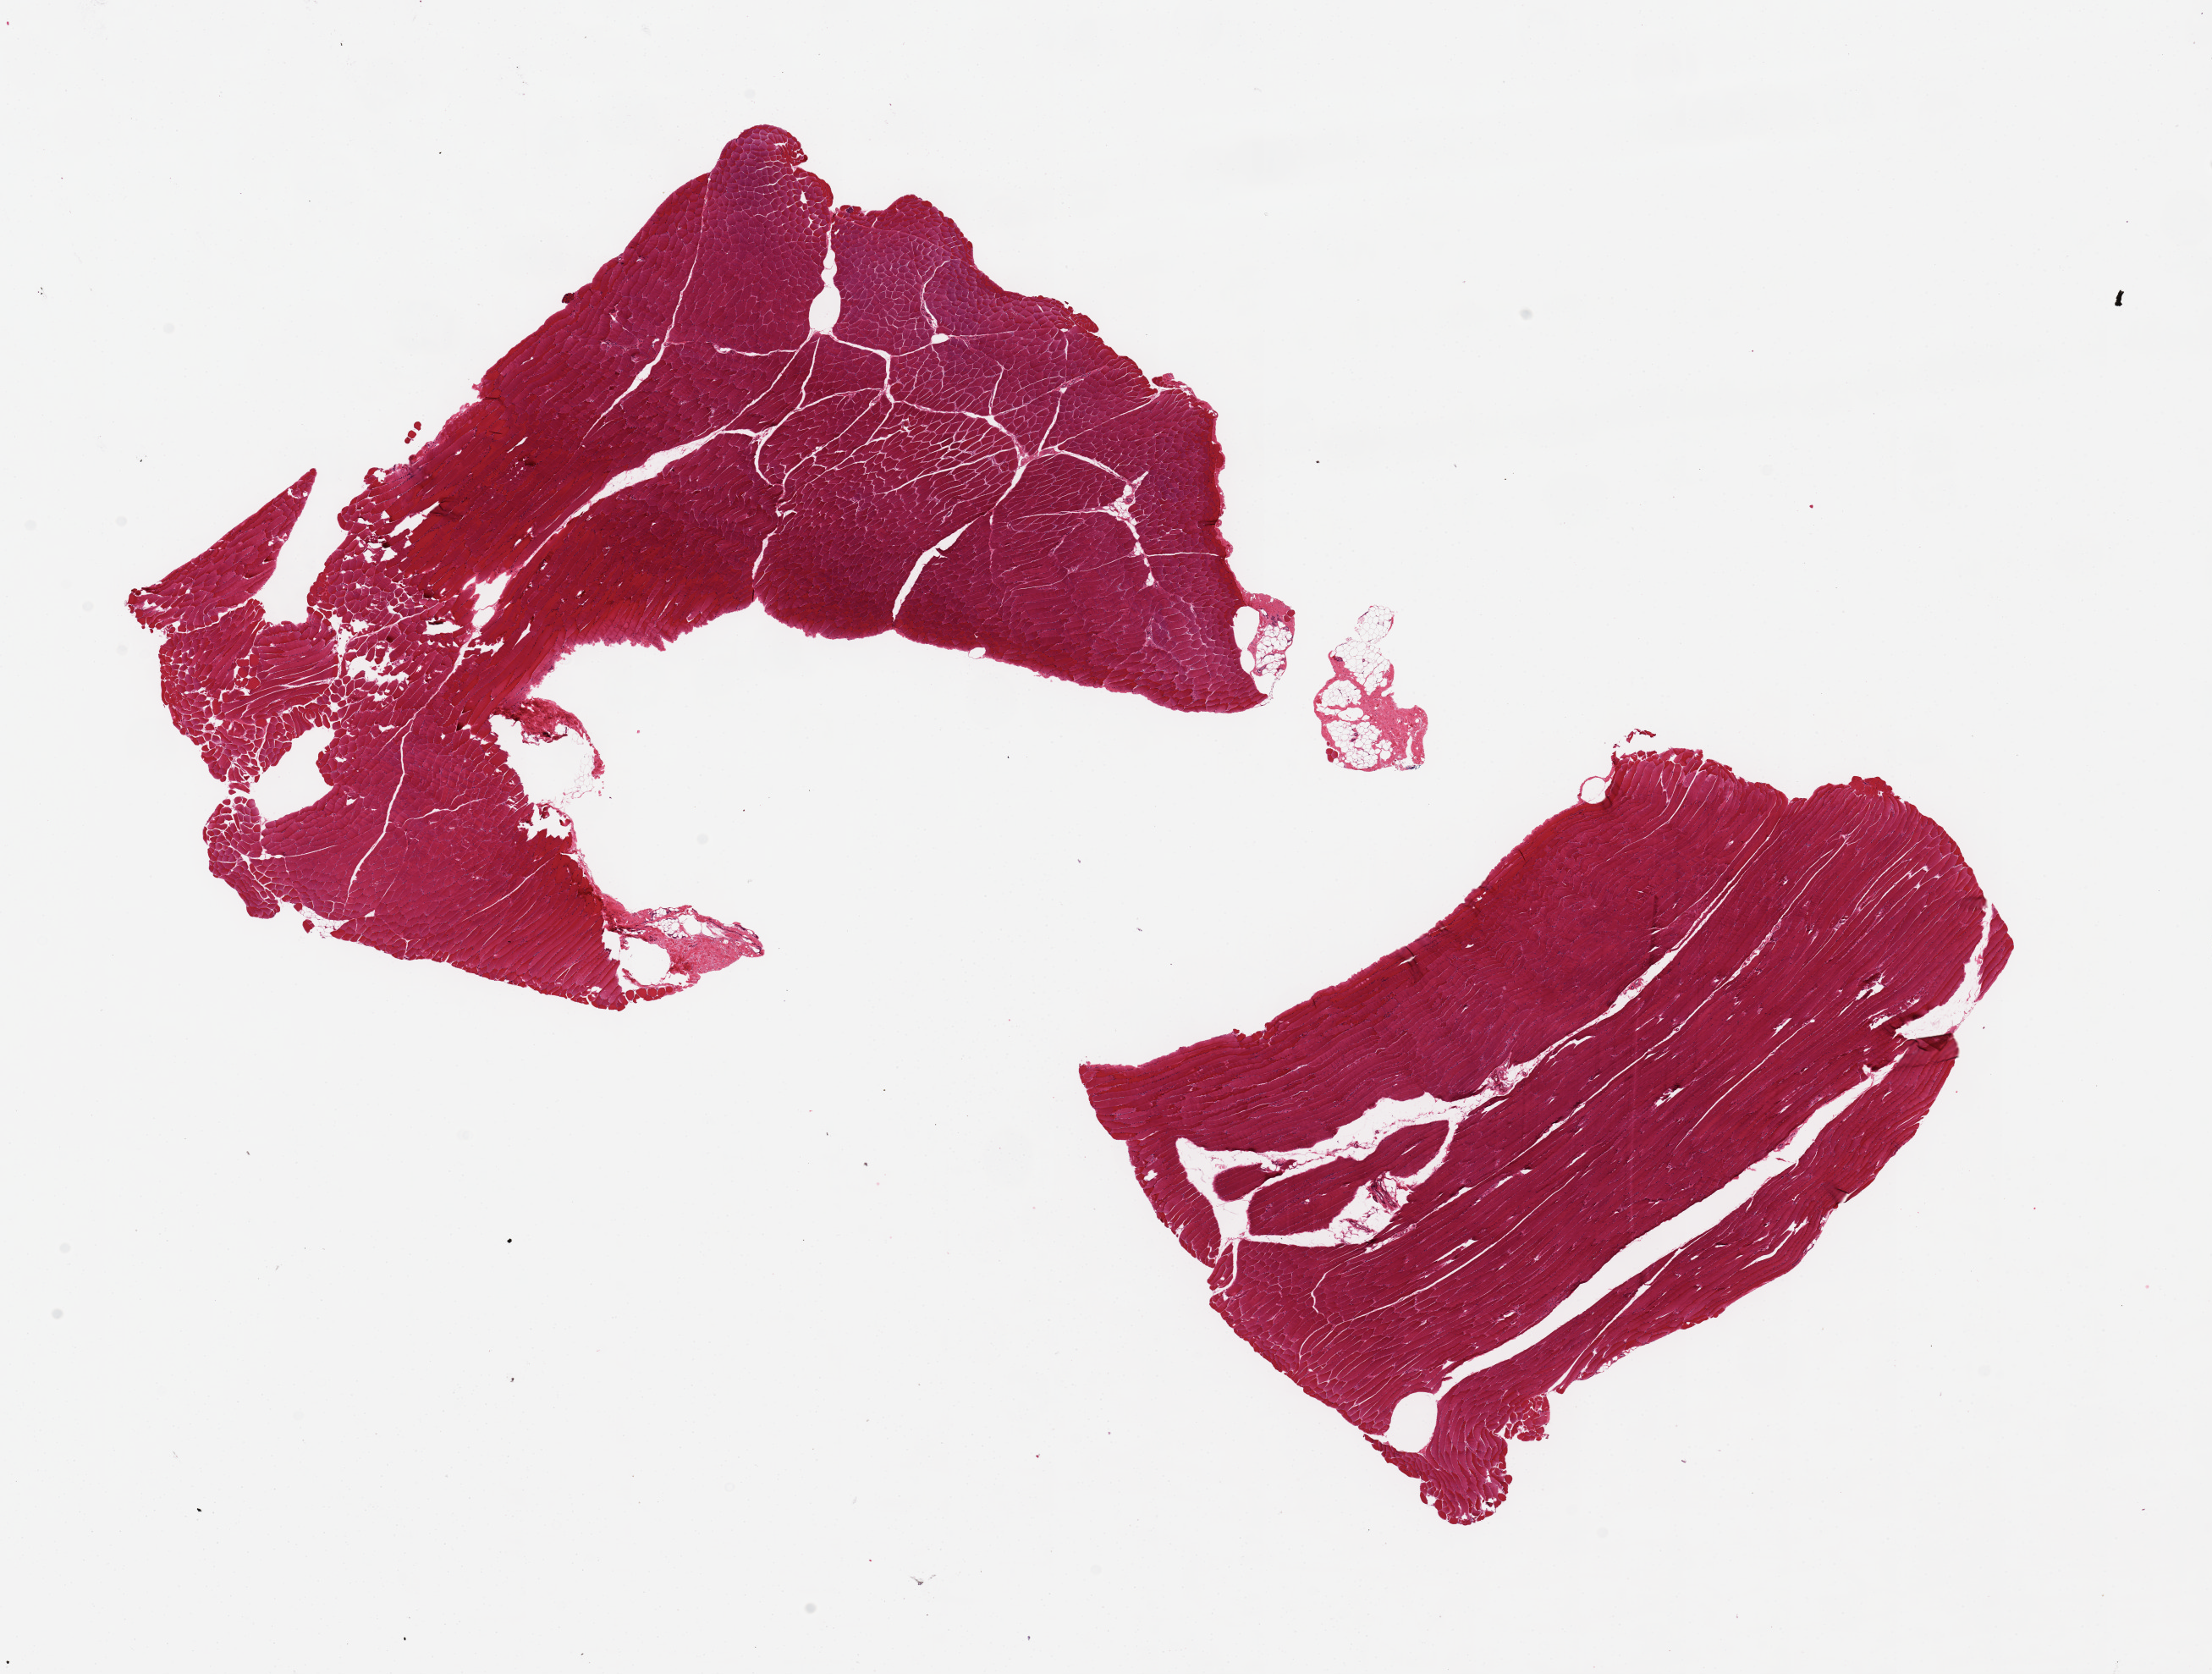
Digitized haematoxylin and eosin-stained section, low-resolution overview of the scanned area, about 20.7 x 15.6 mm (acquisition: 20x scan), PAXgene-fixed paraffin-embedded (PFPE) section, sampled site (target tissue): skeletal muscle, tissue donor sample. Female donor.
• review note (as recorded): 2 pieces, ~8.5x5 mm; focal fragmentation